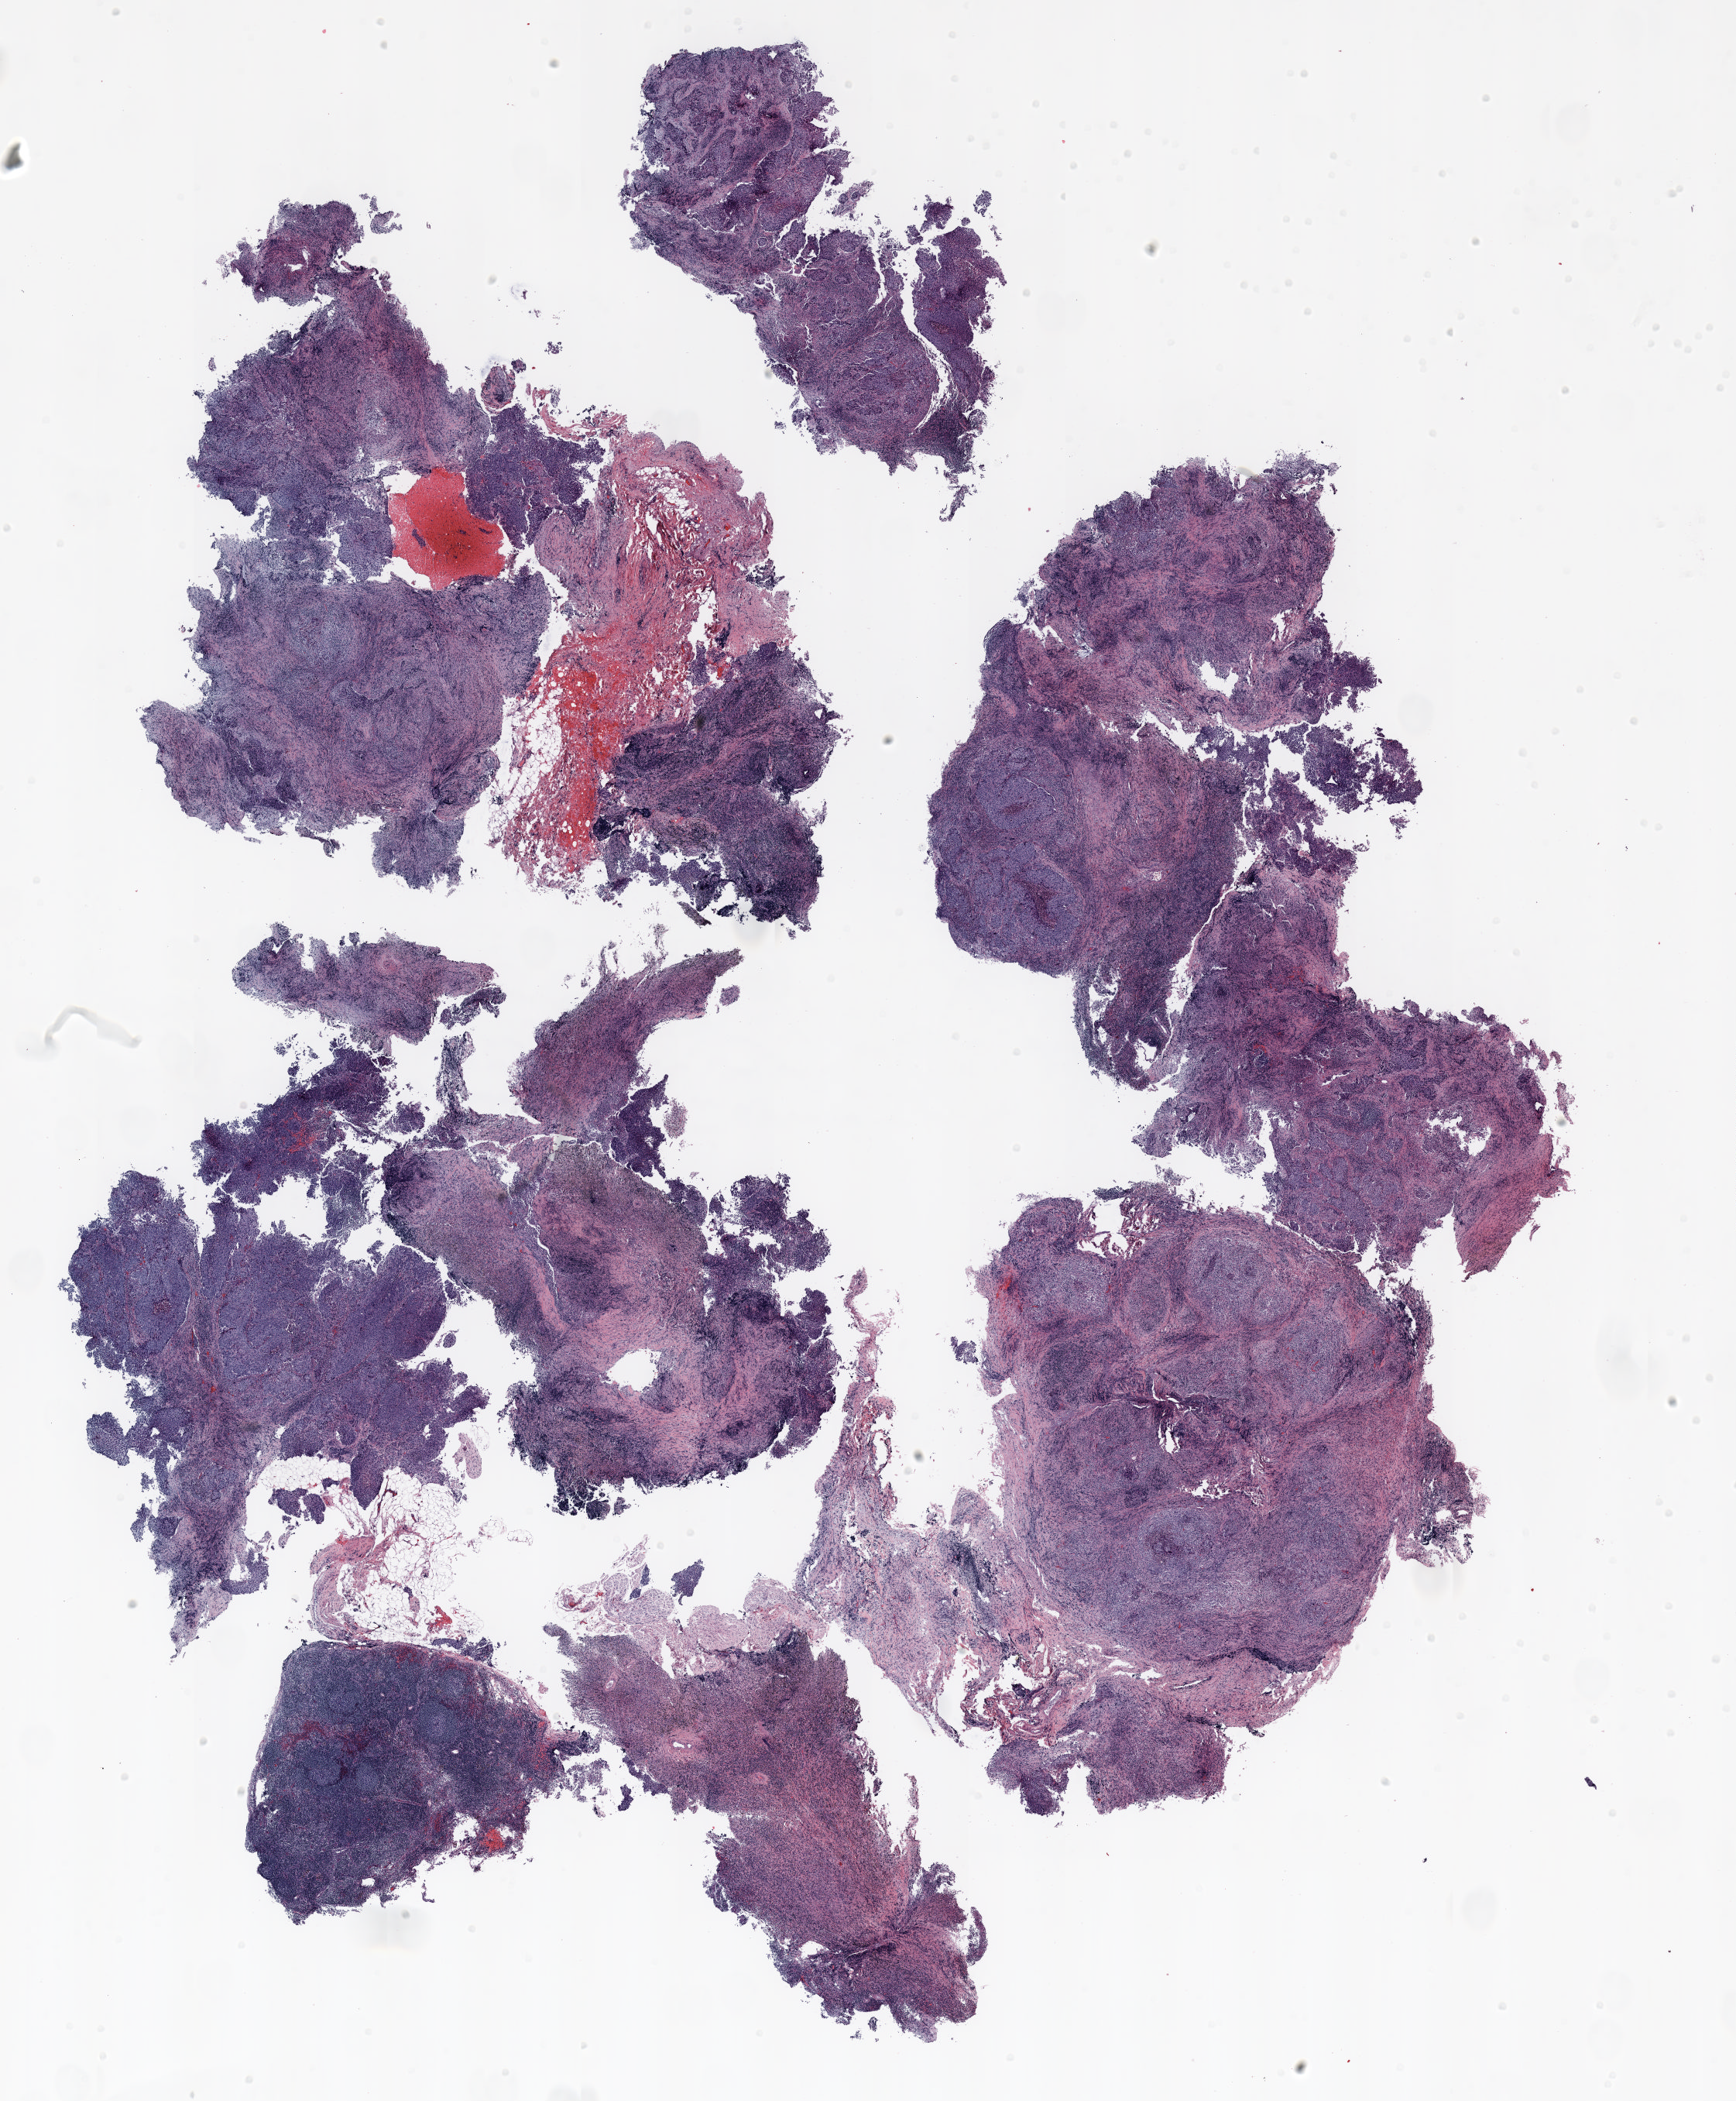
Hematoxylin and eosin (H&E) stained whole-slide image — low-resolution overview of the scanned area, about 18.0 x 21.8 mm (from a 20x scan); formalin-fixed paraffin-embedded (FFPE) section; lung. Female, age 61 at enrolment. Grade: cannot be assessed (GX).
Primary tumour location (clinical record): right upper lobe. Participant's lung-cancer diagnosis: Squamous cell carcinoma, NOS. Stage (AJCC 6th edition): IIIA. Tumour size (pathology): 8 mm.